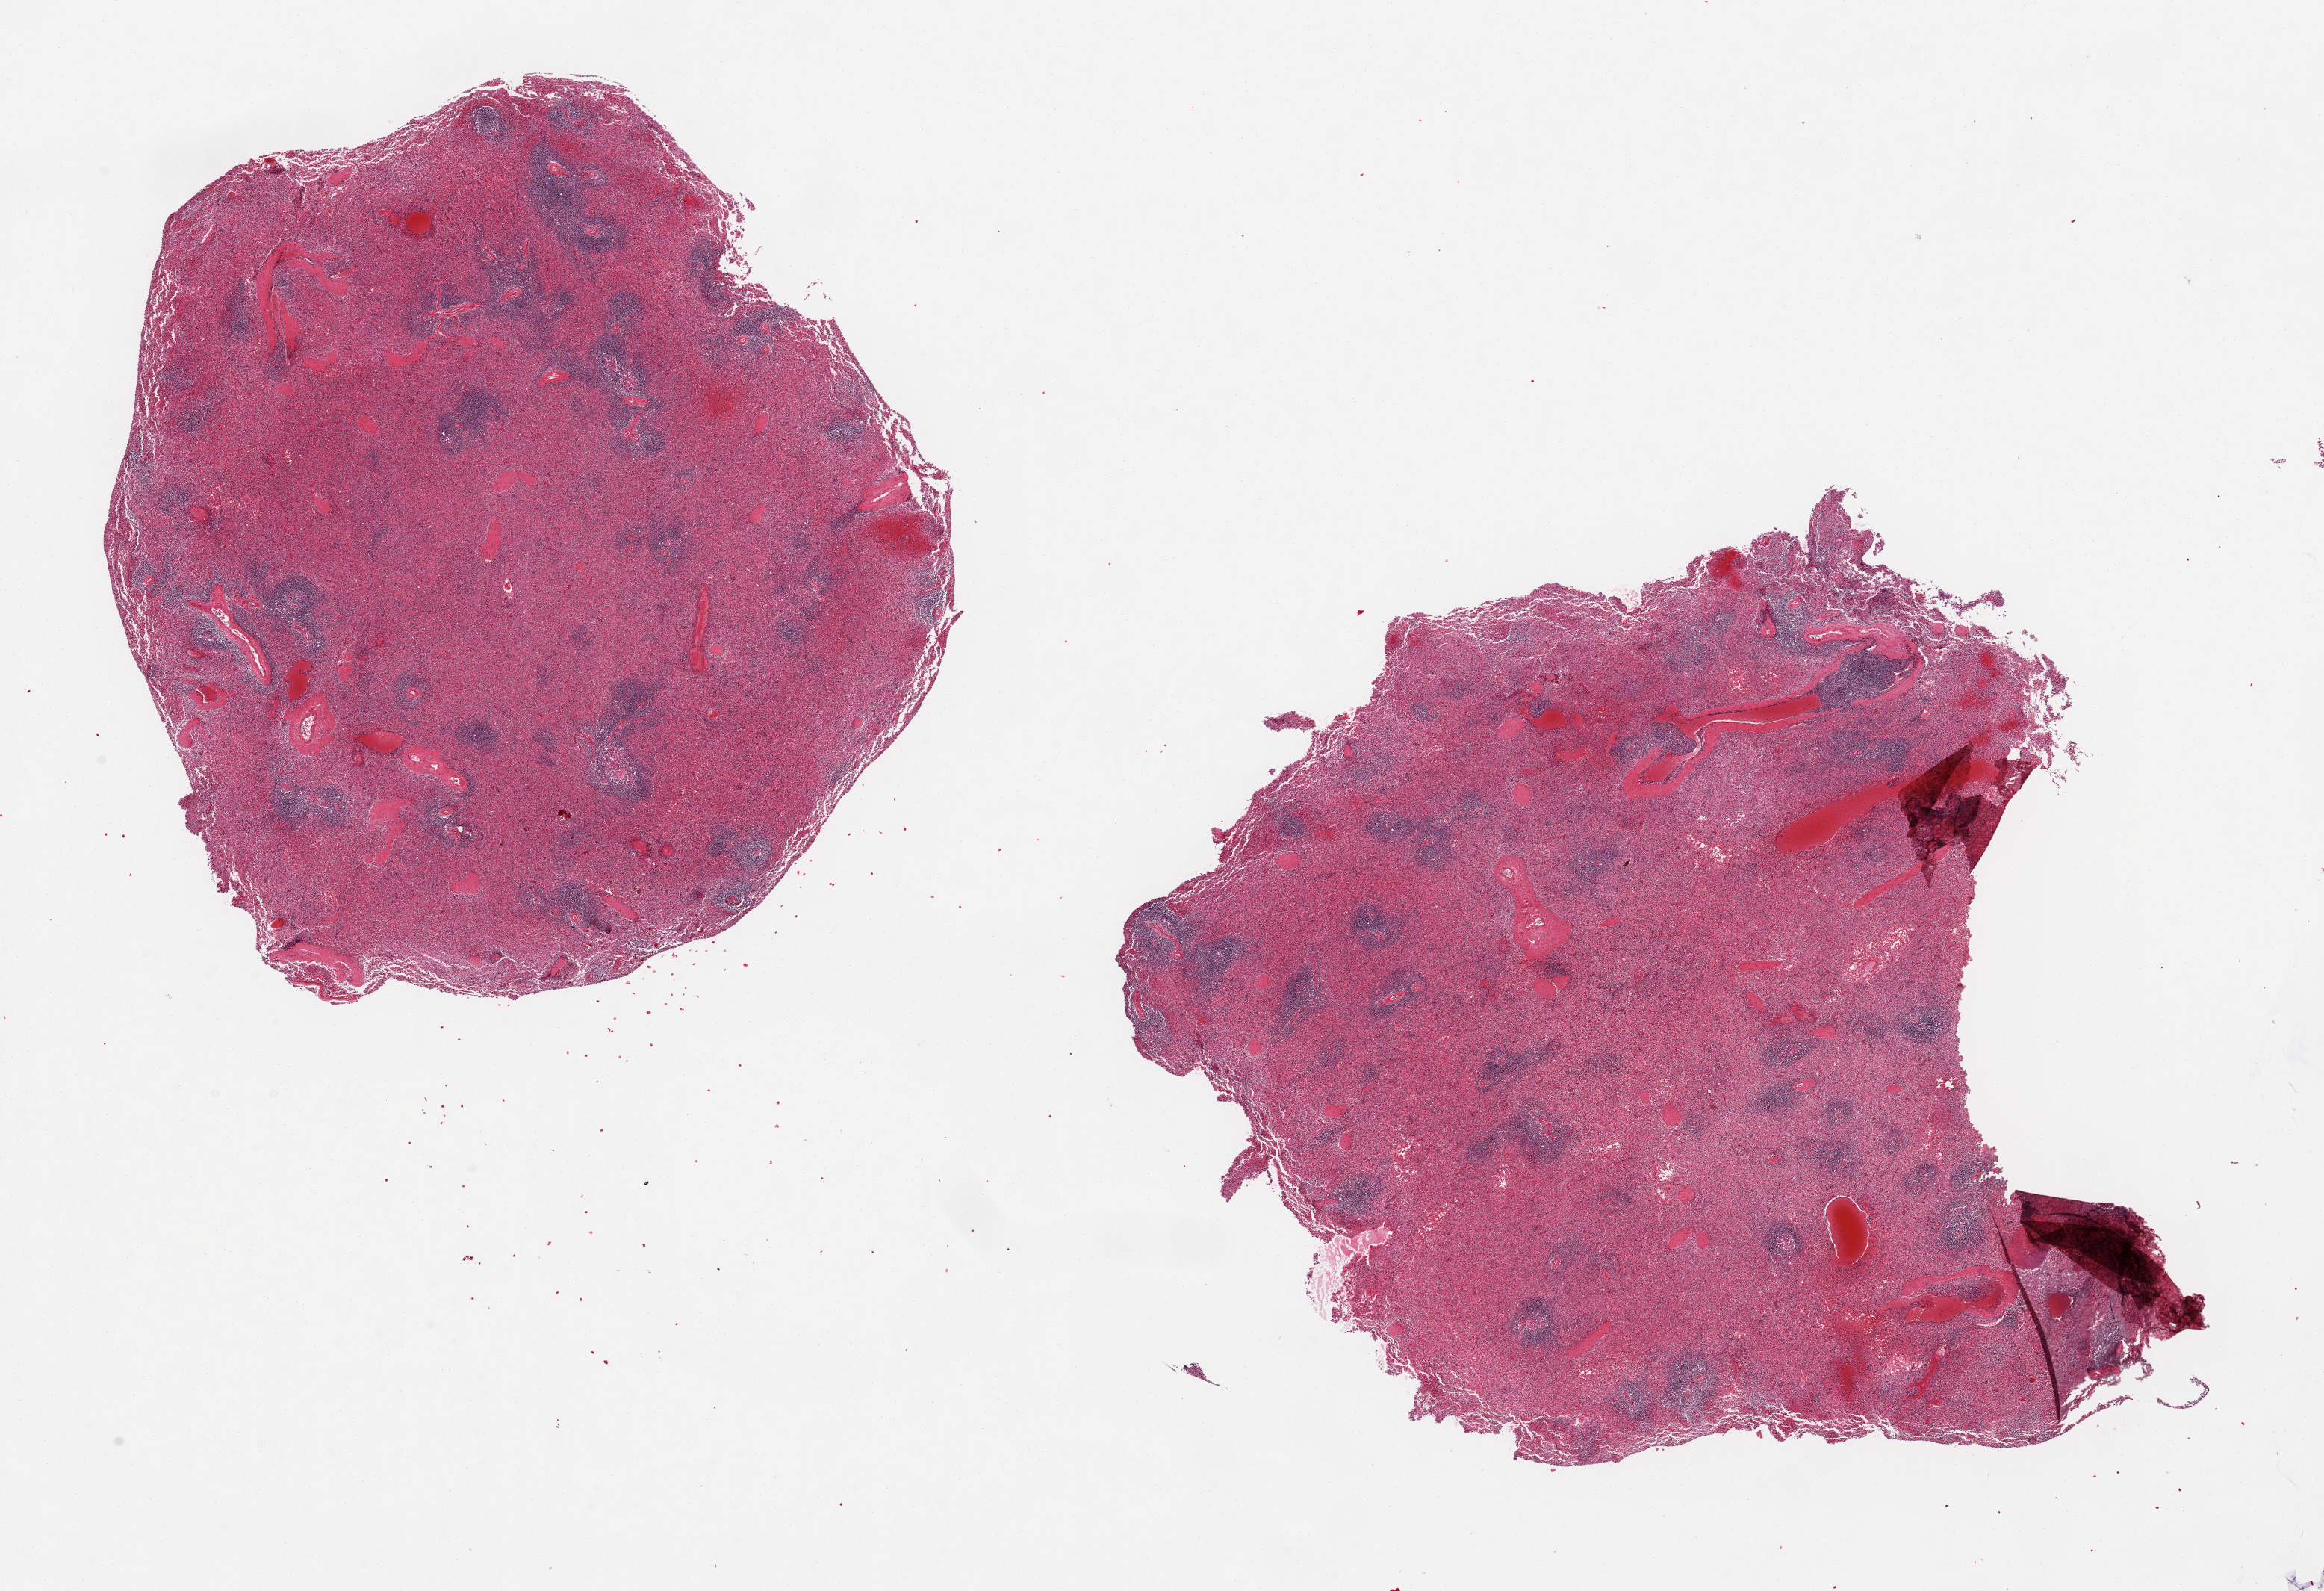
Whole-slide image, H&E stain, low-resolution overview of the scanned area, about 24.6 x 16.8 mm (acquisition: 20x scan), PAXgene-fixed, paraffin-embedded tissue, section of spleen (target tissue), donor tissue sample.
Reviewer comment on this tissue sample: 2 pieces, 9x9 &9x8 mm.